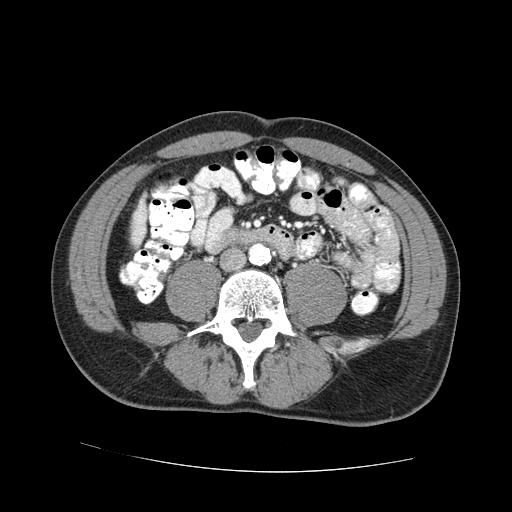
Contrast-enhanced abdominal CT (liver protocol), one axial slice. 100 kVp. One of 2 acquisitions stored at this slice position. Soft-tissue window (W 400 / L 40 HU). 2.5 mm slice thickness. 512 × 512 image matrix, field of view 380 × 380 mm. From the clinical record (not read from this slice): diagnosis: hepatocellular carcinoma (patient treated with transarterial chemoembolisation; whether this scan precedes or follows treatment is not stated here); TNM stage (as recorded): Stage-IVA; Child-Pugh class: A; tumour differentiation: no biopsy; tumour nodularity: uninodular.
Outlined on this slice (semi-automatically segmented with operator editing):
- liver parenchyma outside the tumour (the mass and vessels are separate outlines, so this box may not span the whole liver): box from (x=132, y=200) to (x=146, y=244) px